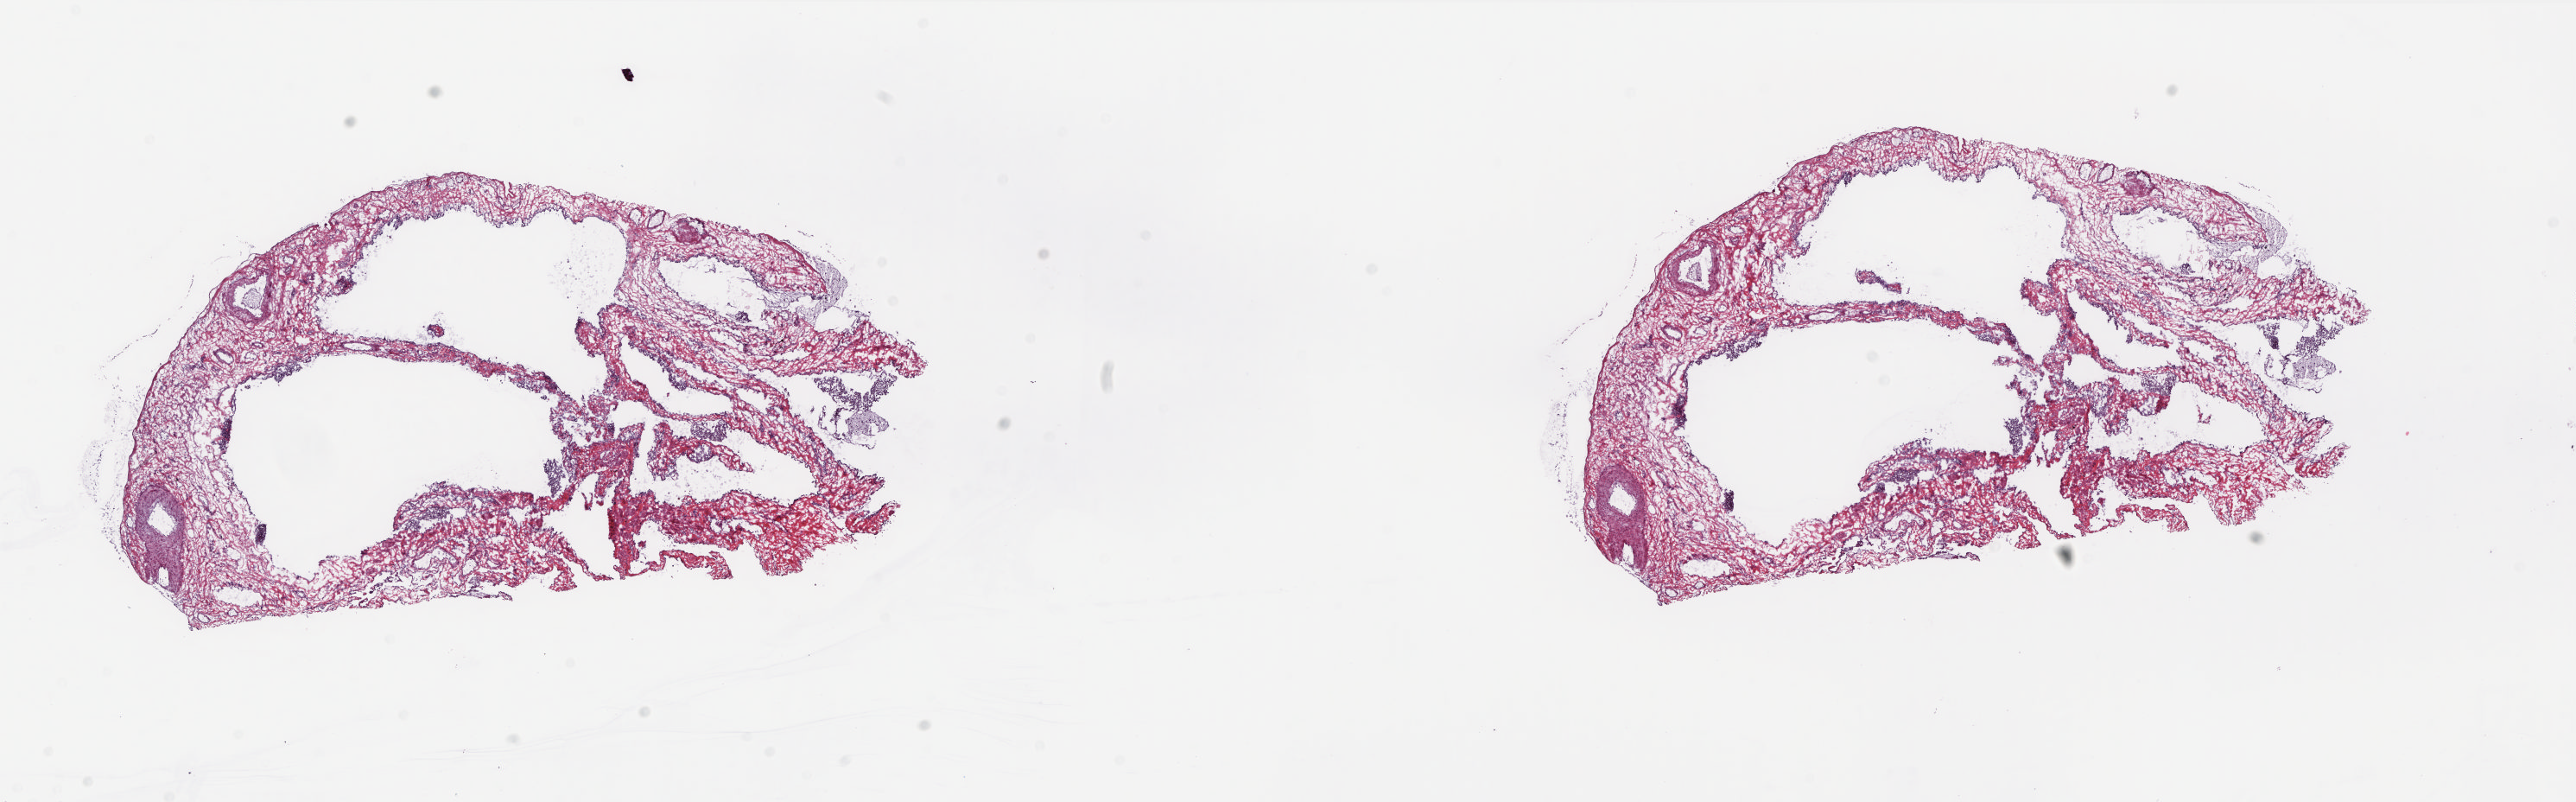
Hematoxylin and eosin (H&E) stained whole-slide image — shown as a low-resolution overview of the whole scanned area (about 24.0 x 7.5 mm, from a 20x scan). Frozen section from the top of the tissue portion. Lung, solid tissue normal (non-tumour tissue) sample. Male, age 43 years at initial diagnosis. Composition of this section per pathologist review: tumour cells 0%, tumour nuclei 0%, normal cells 100%, stromal cells 0%, necrosis 0%. Inflammatory infiltration, as recorded: lymphocyte infiltration 20%, monocyte infiltration 20%, neutrophil infiltration 40%.
This section: solid tissue normal sample (biorepository sample class). Patient diagnosis: Adenocarcinoma, NOS (upper lobe, lung).